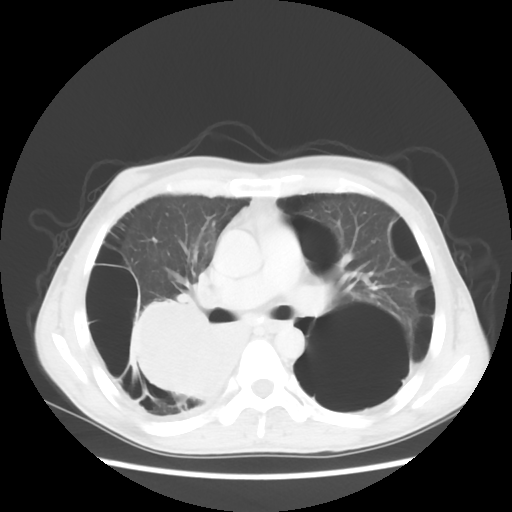
Chest CT, one axial slice. Position 32 of 56 along the scan axis. Reconstruction kernel STANDARD. 140 kVp. Lung window (W 1500 / L -600 HU). 5 mm slice thickness. 512 × 512 image matrix, field of view 351 × 351 mm. Male patient, age 41 years. Case-level facts recorded for this patient, not image findings: clinical TNM (as recorded): T4 N0 M1a; histopathological grade: G3.
Outlined on this slice (rectangle marked by the reading radiologist):
- lung tumour (recorded histology: large cell carcinoma): box from (x=126, y=289) to (x=252, y=414) px